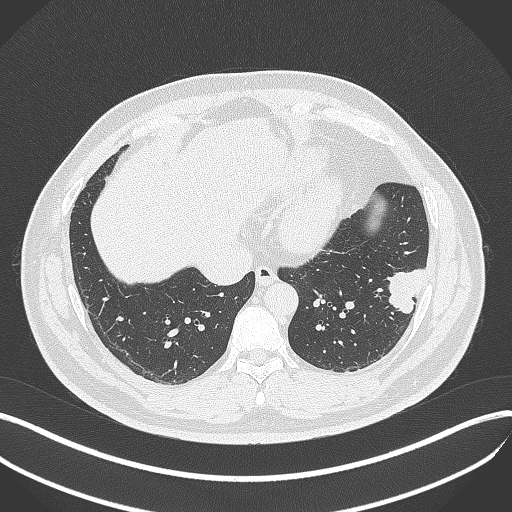
Chest CT, one axial slice; position 130 of 429 along the scan axis; reconstruction kernel B70f; 120 kVp; lung window (W 1500 / L -600 HU); 1 mm slice thickness; 512 × 512 image matrix, field of view 400 × 400 mm. Patient: male, 39 years. Case-level facts recorded for this patient, not image findings: clinical TNM (as recorded): T2a N0 M0; histopathological grade: G2-3.
Structures marked on this image (rectangle marked by the reading radiologist):
- lung tumour (recorded histology: adenocarcinoma): bounding box <376,262,436,316> (left, top, right, bottom; pixels)